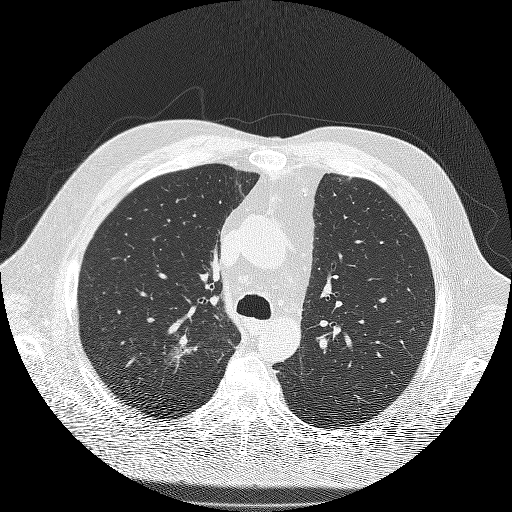
Low-dose screening chest CT, one axial slice; slice 138 of 180 in the series (ordered by position); reconstruction kernel FC51; lung window (W 1500 / L -600 HU); 512 × 512 image matrix, field of view 385 × 385 mm.
Annotated regions visible in this slice (outlined manually by an expert reader):
- lesion 1 (tumor, upper lobe of right lung): bounding box <171,335,198,367> (left, top, right, bottom; pixels)